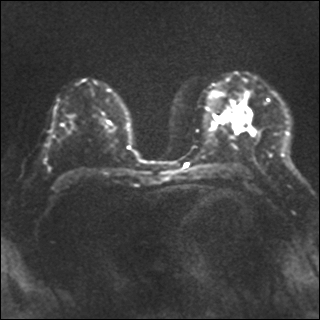
Breast MRI, one axial slice; slice 22 of 40 in the series (ordered by position); diffusion-weighted series; image 2 of 4 stored at this slice position (different b-values; order by instance number); 1.5 T; 4 mm slice thickness; 320 × 320 image matrix, field of view 320 × 320 mm. Female patient.
Outlined on this slice (expert manual segmentation):
- tumour on diffusion-weighted imaging: box from (x=235, y=116) to (x=246, y=128) px